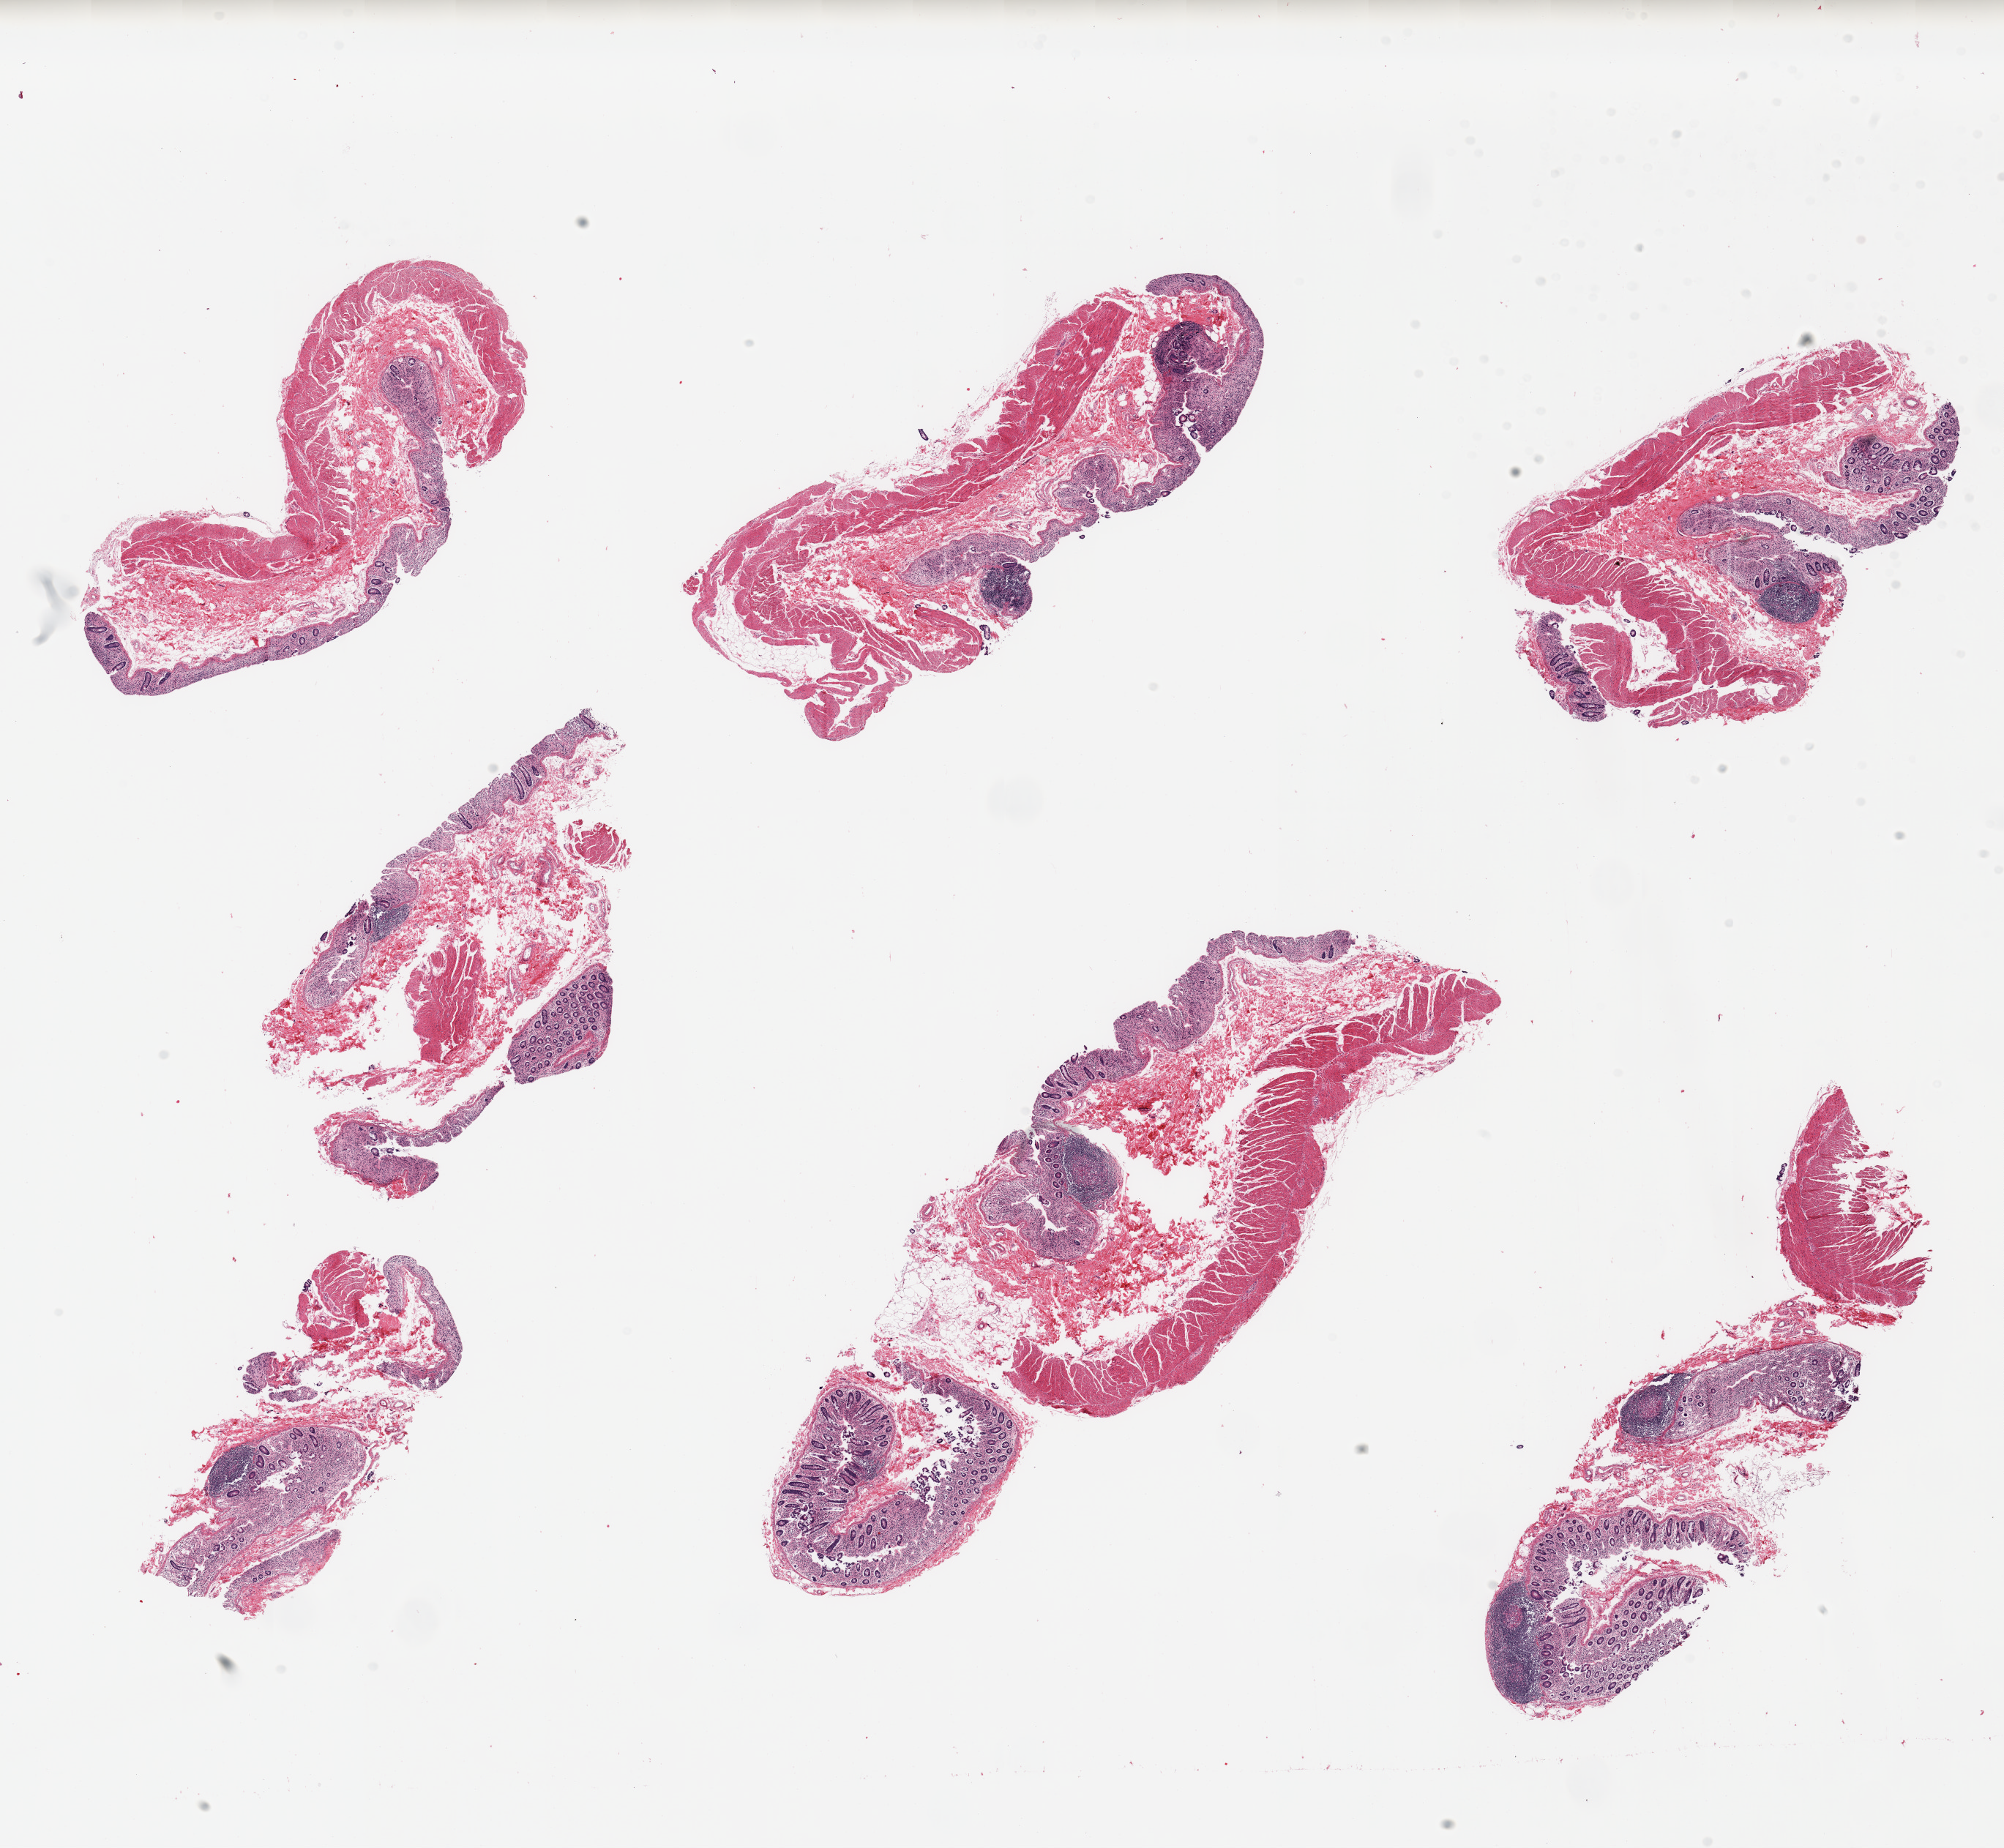
Digitized hematoxylin and eosin (H&E)-stained section, brightfield, whole scanned area (about 21.7 x 20.0 mm, acquisition: 20x scan) shown as a low-resolution overview; PAXgene-fixed paraffin-embedded (PFPE) section; sampled site (target tissue): transverse colon; donor tissue sample. Male donor.
Reviewer comment on this tissue sample: 6 pieces, mucosa up to 0.3mm, totally autolyzed.